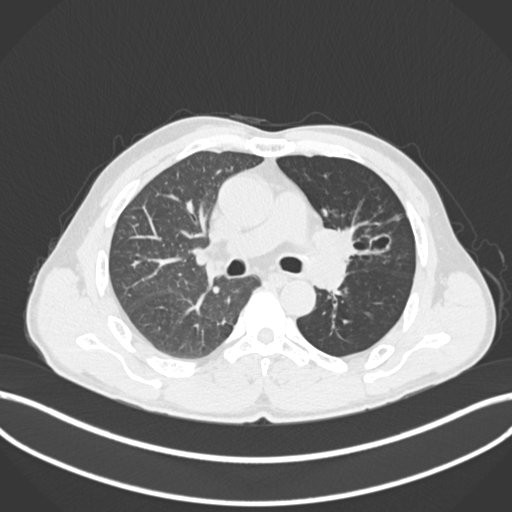
Chest CT, one axial slice. Slice 114 of 255 in the series (ordered by position). Reconstruction kernel B30f. 120 kVp. Lung window (W 1500 / L -600 HU). 512 × 512 image matrix, field of view 400 × 400 mm. Male patient, age 57 years. From the clinical record (not read from this slice): clinical TNM (as recorded): T2b N0 M0.
Annotated regions visible in this slice (rectangle marked by the reading radiologist):
- lung tumour (recorded histology: squamous cell carcinoma): bounding box (x1, y1, x2, y2) in pixels: (313, 220, 370, 261)